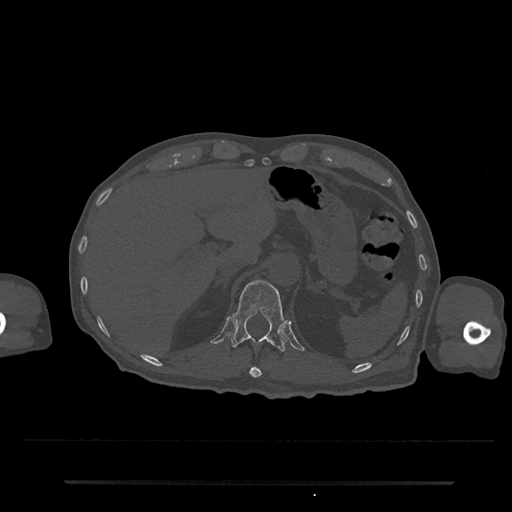
CT including the spine, one axial slice. Position 205 of 797 along the scan axis. Reconstruction kernel Br40s/3. 120 kVp. Bone window (W 1800 / L 400 HU). 512 × 512 image matrix. Patient: male, 74 years. Case-level facts recorded for this patient, not image findings: primary cancer: prostate.
Structures marked on this image (semi-automatic segmentation, software-assisted and operator-edited):
- T11 vertebra: bounding box (x1, y1, x2, y2) in pixels: (249, 366, 262, 378)
- T12 vertebra: (228, 280, 287, 352)